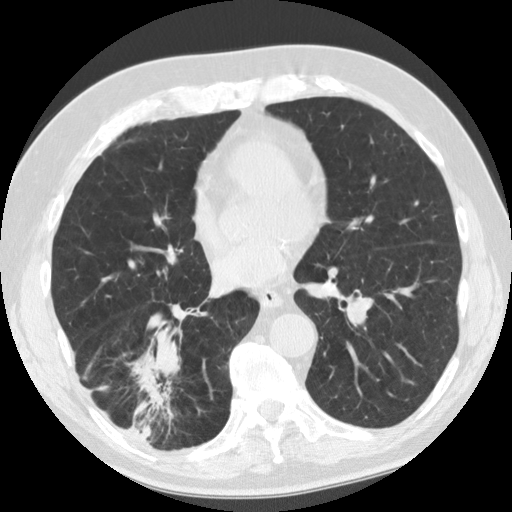
Axial slice from a low-dose chest CT screening exam. First (baseline) screen. Lung window (W 1500 / L -600 HU). Standard (soft-tissue) reconstruction kernel (STANDARD). 512 × 512 image matrix. Male, age 69 years at enrolment.
Expert-annotated lung lesion, bounding box <113,333,199,441> (left, top, right, bottom; pixels). The screening reader recorded 2 non-calcified nodules or masses ≥4 mm on this exam (right lower lobe, right lower lobe); which of them this box marks is not recorded. Official screen result: positive, change unspecified: nodule(s) >= 4 mm or enlarging nodule(s), mass(es), or other non-specific abnormalities suspicious for lung cancer. Later outcome: lung cancer diagnosed 40 days after this screen — adenocarcinoma, NOS, right lower lobe, stage IIB (AJCC 6th edition), 45 mm at pathology.